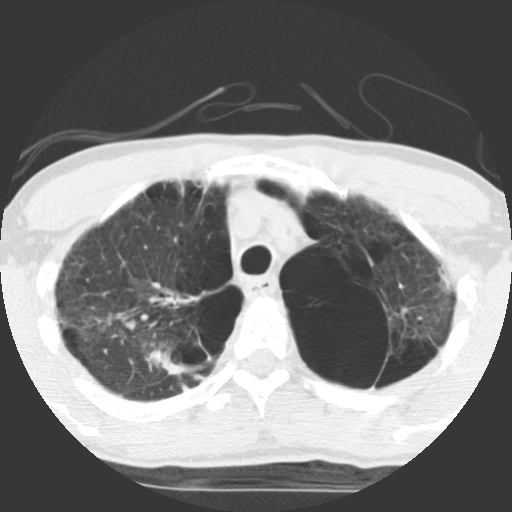
Chest CT (low-dose screening protocol), one axial image. Baseline screening round. Lung window (W 1500 / L -600 HU). 140 kVp. Male, age 62 years at enrolment. Current smoker at enrolment.
• Expert-annotated lung lesion, bounding box [x1, y1, x2, y2] px = [119, 322, 213, 391].
• No non-calcified nodule or mass ≥4 mm was recorded by the screening reader at this exam.
• Official screen result: negative screen, minor abnormalities not suspicious for lung cancer.
• Lung cancer was diagnosed 357 days after this screen: non-small cell carcinoma, right upper lobe, poorly differentiated (G3), stage IA (AJCC 6th edition), 70 mm at pathology.